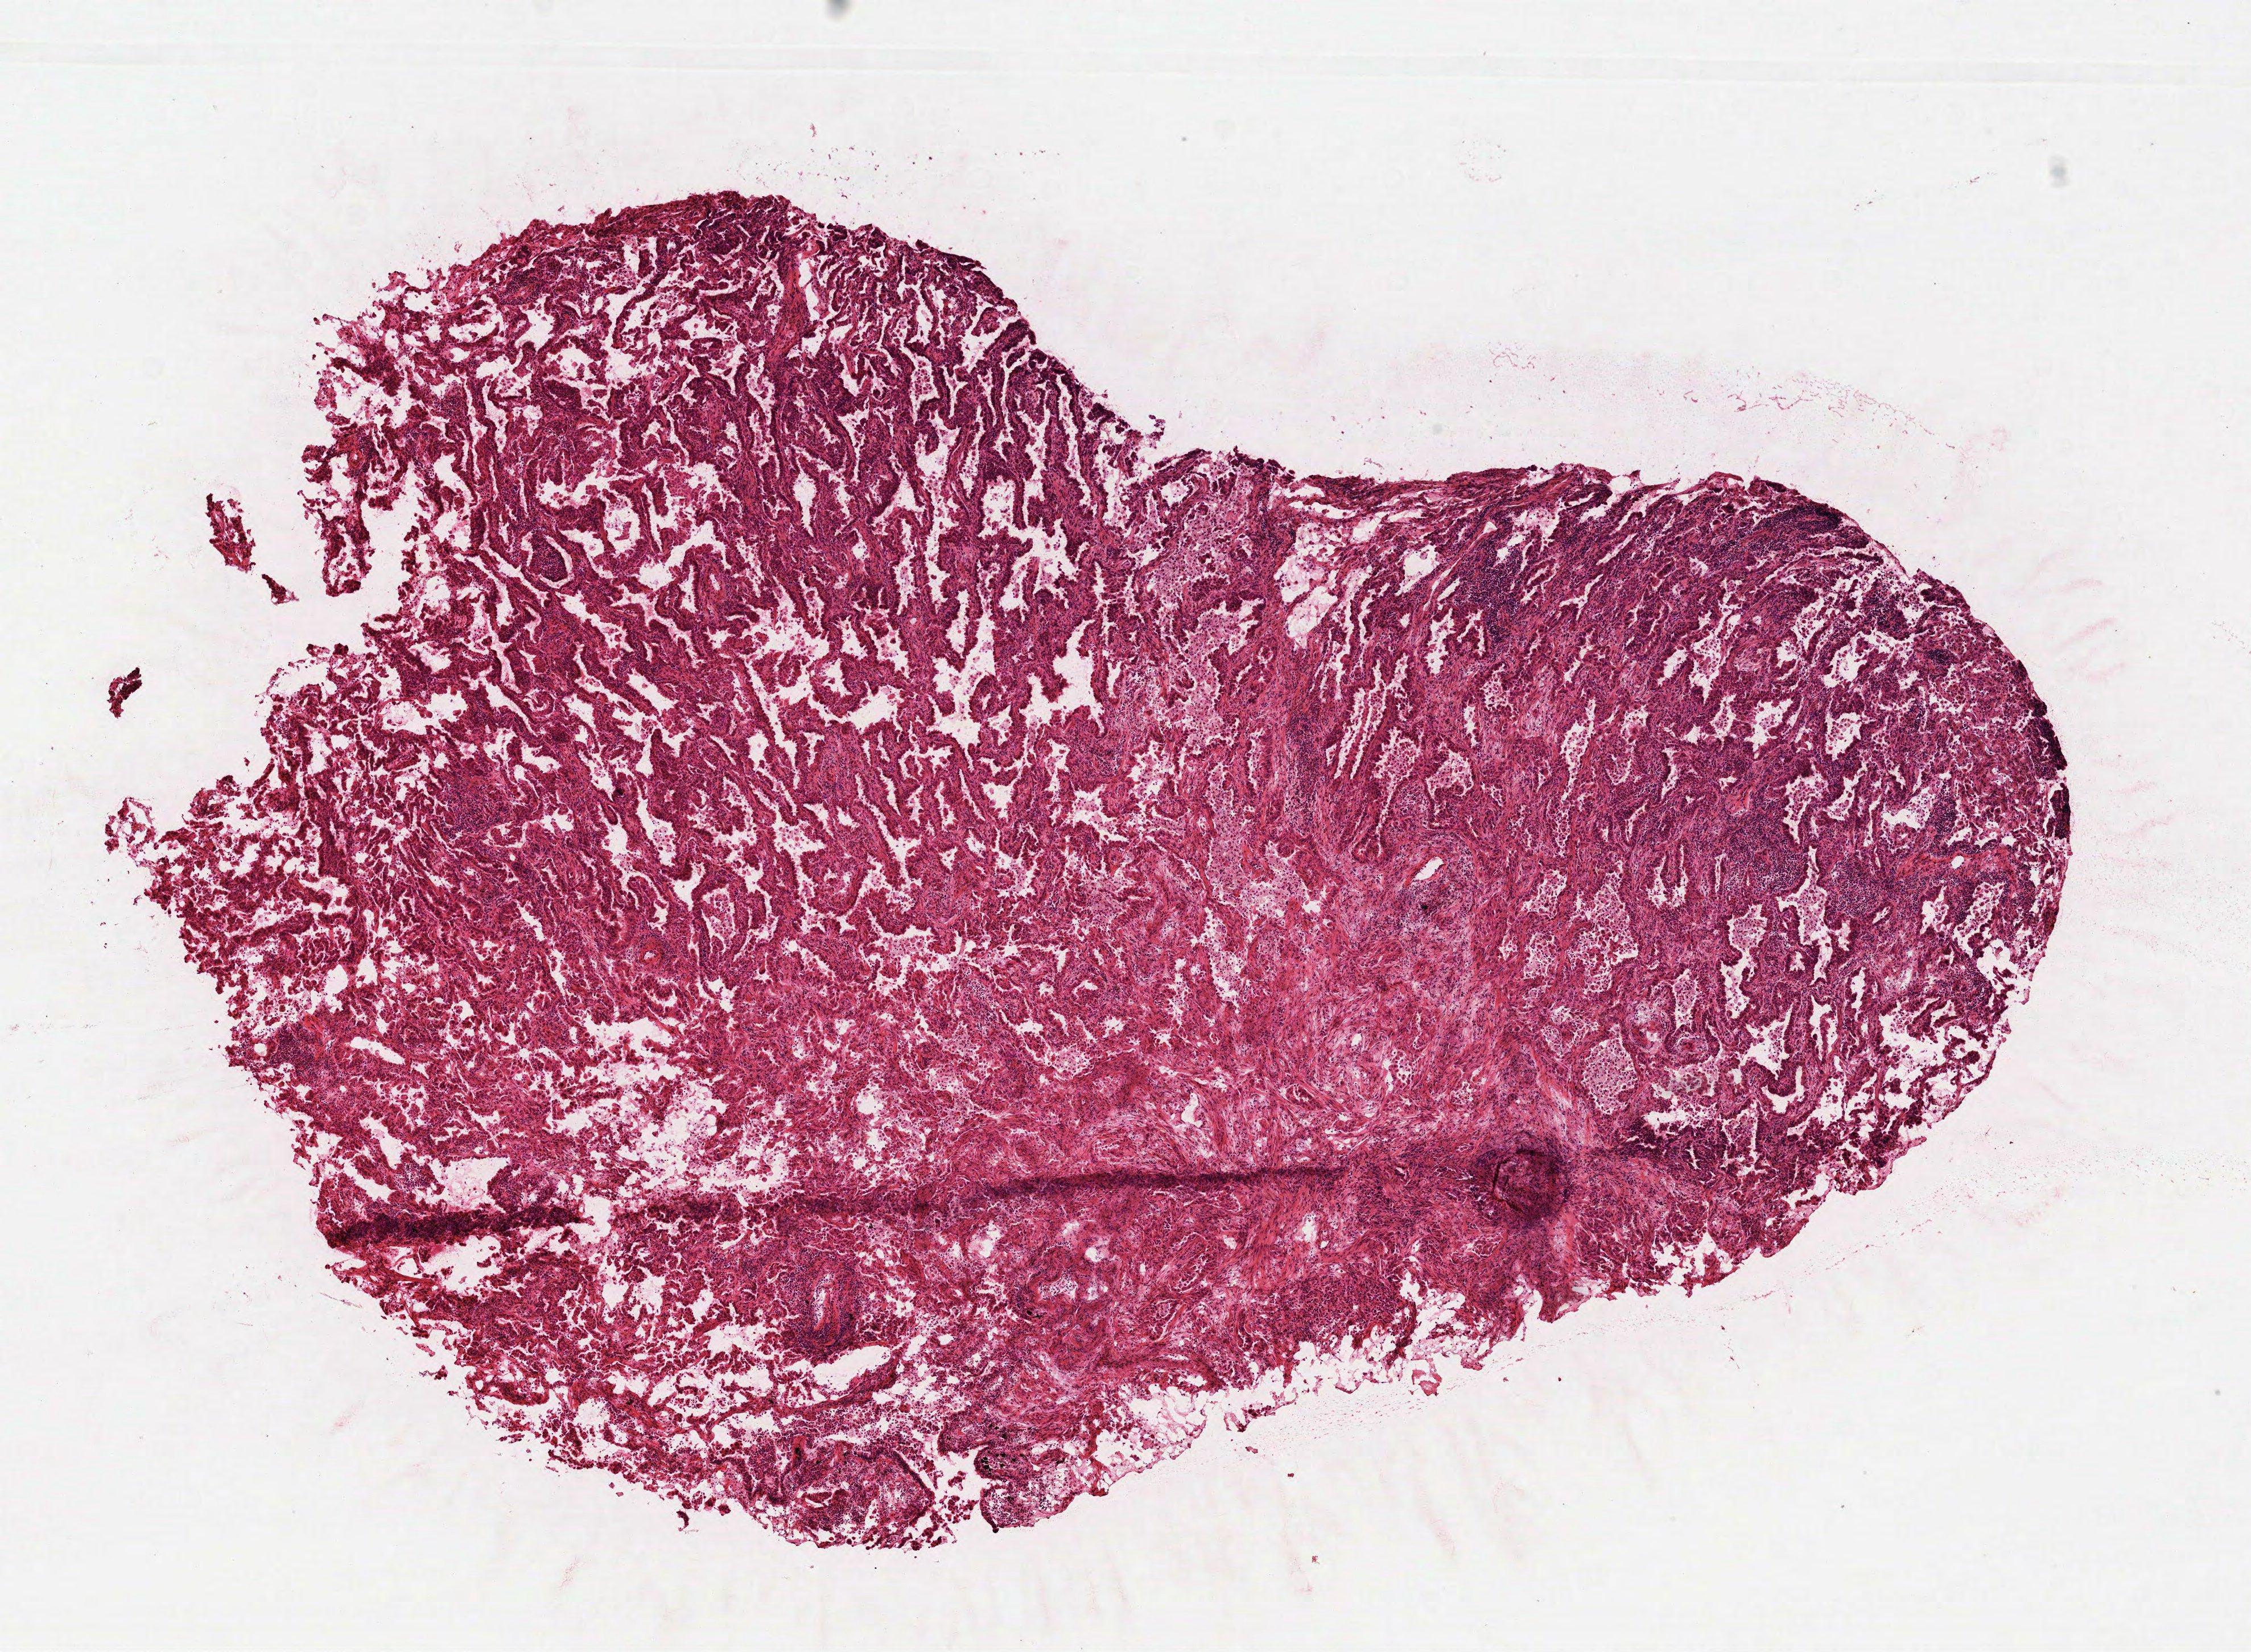
H&E-stained whole-slide image — a low-resolution overview of the entire scanned area, about 8.0 x 5.9 mm (acquisition: 40x scan), formalin-fixed paraffin-embedded (FFPE) diagnostic section, primary tumour sample from the lung. Male, age 72 years at initial diagnosis.
AJCC pathologic stage: IA (7th edition). Laterality: right. Diagnosis: Acinar cell carcinoma.